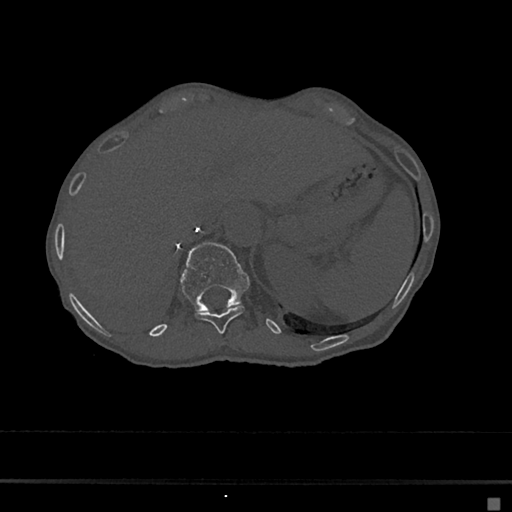
CT including the spine, one axial slice. Reconstruction kernel Br40s/3. Bone window (W 1800 / L 400 HU). 0.5 mm slice thickness. 512 × 512 image matrix, field of view 360 × 360 mm. Patient: female, 68 years. Case-level facts recorded for this patient, not image findings: primary cancer: renal.
Outlined on this slice (semi-automatically segmented with operator editing):
- T11 vertebra: bounding box <195,304,245,334> (left, top, right, bottom; pixels)
- T12 vertebra: <180,243,249,311>